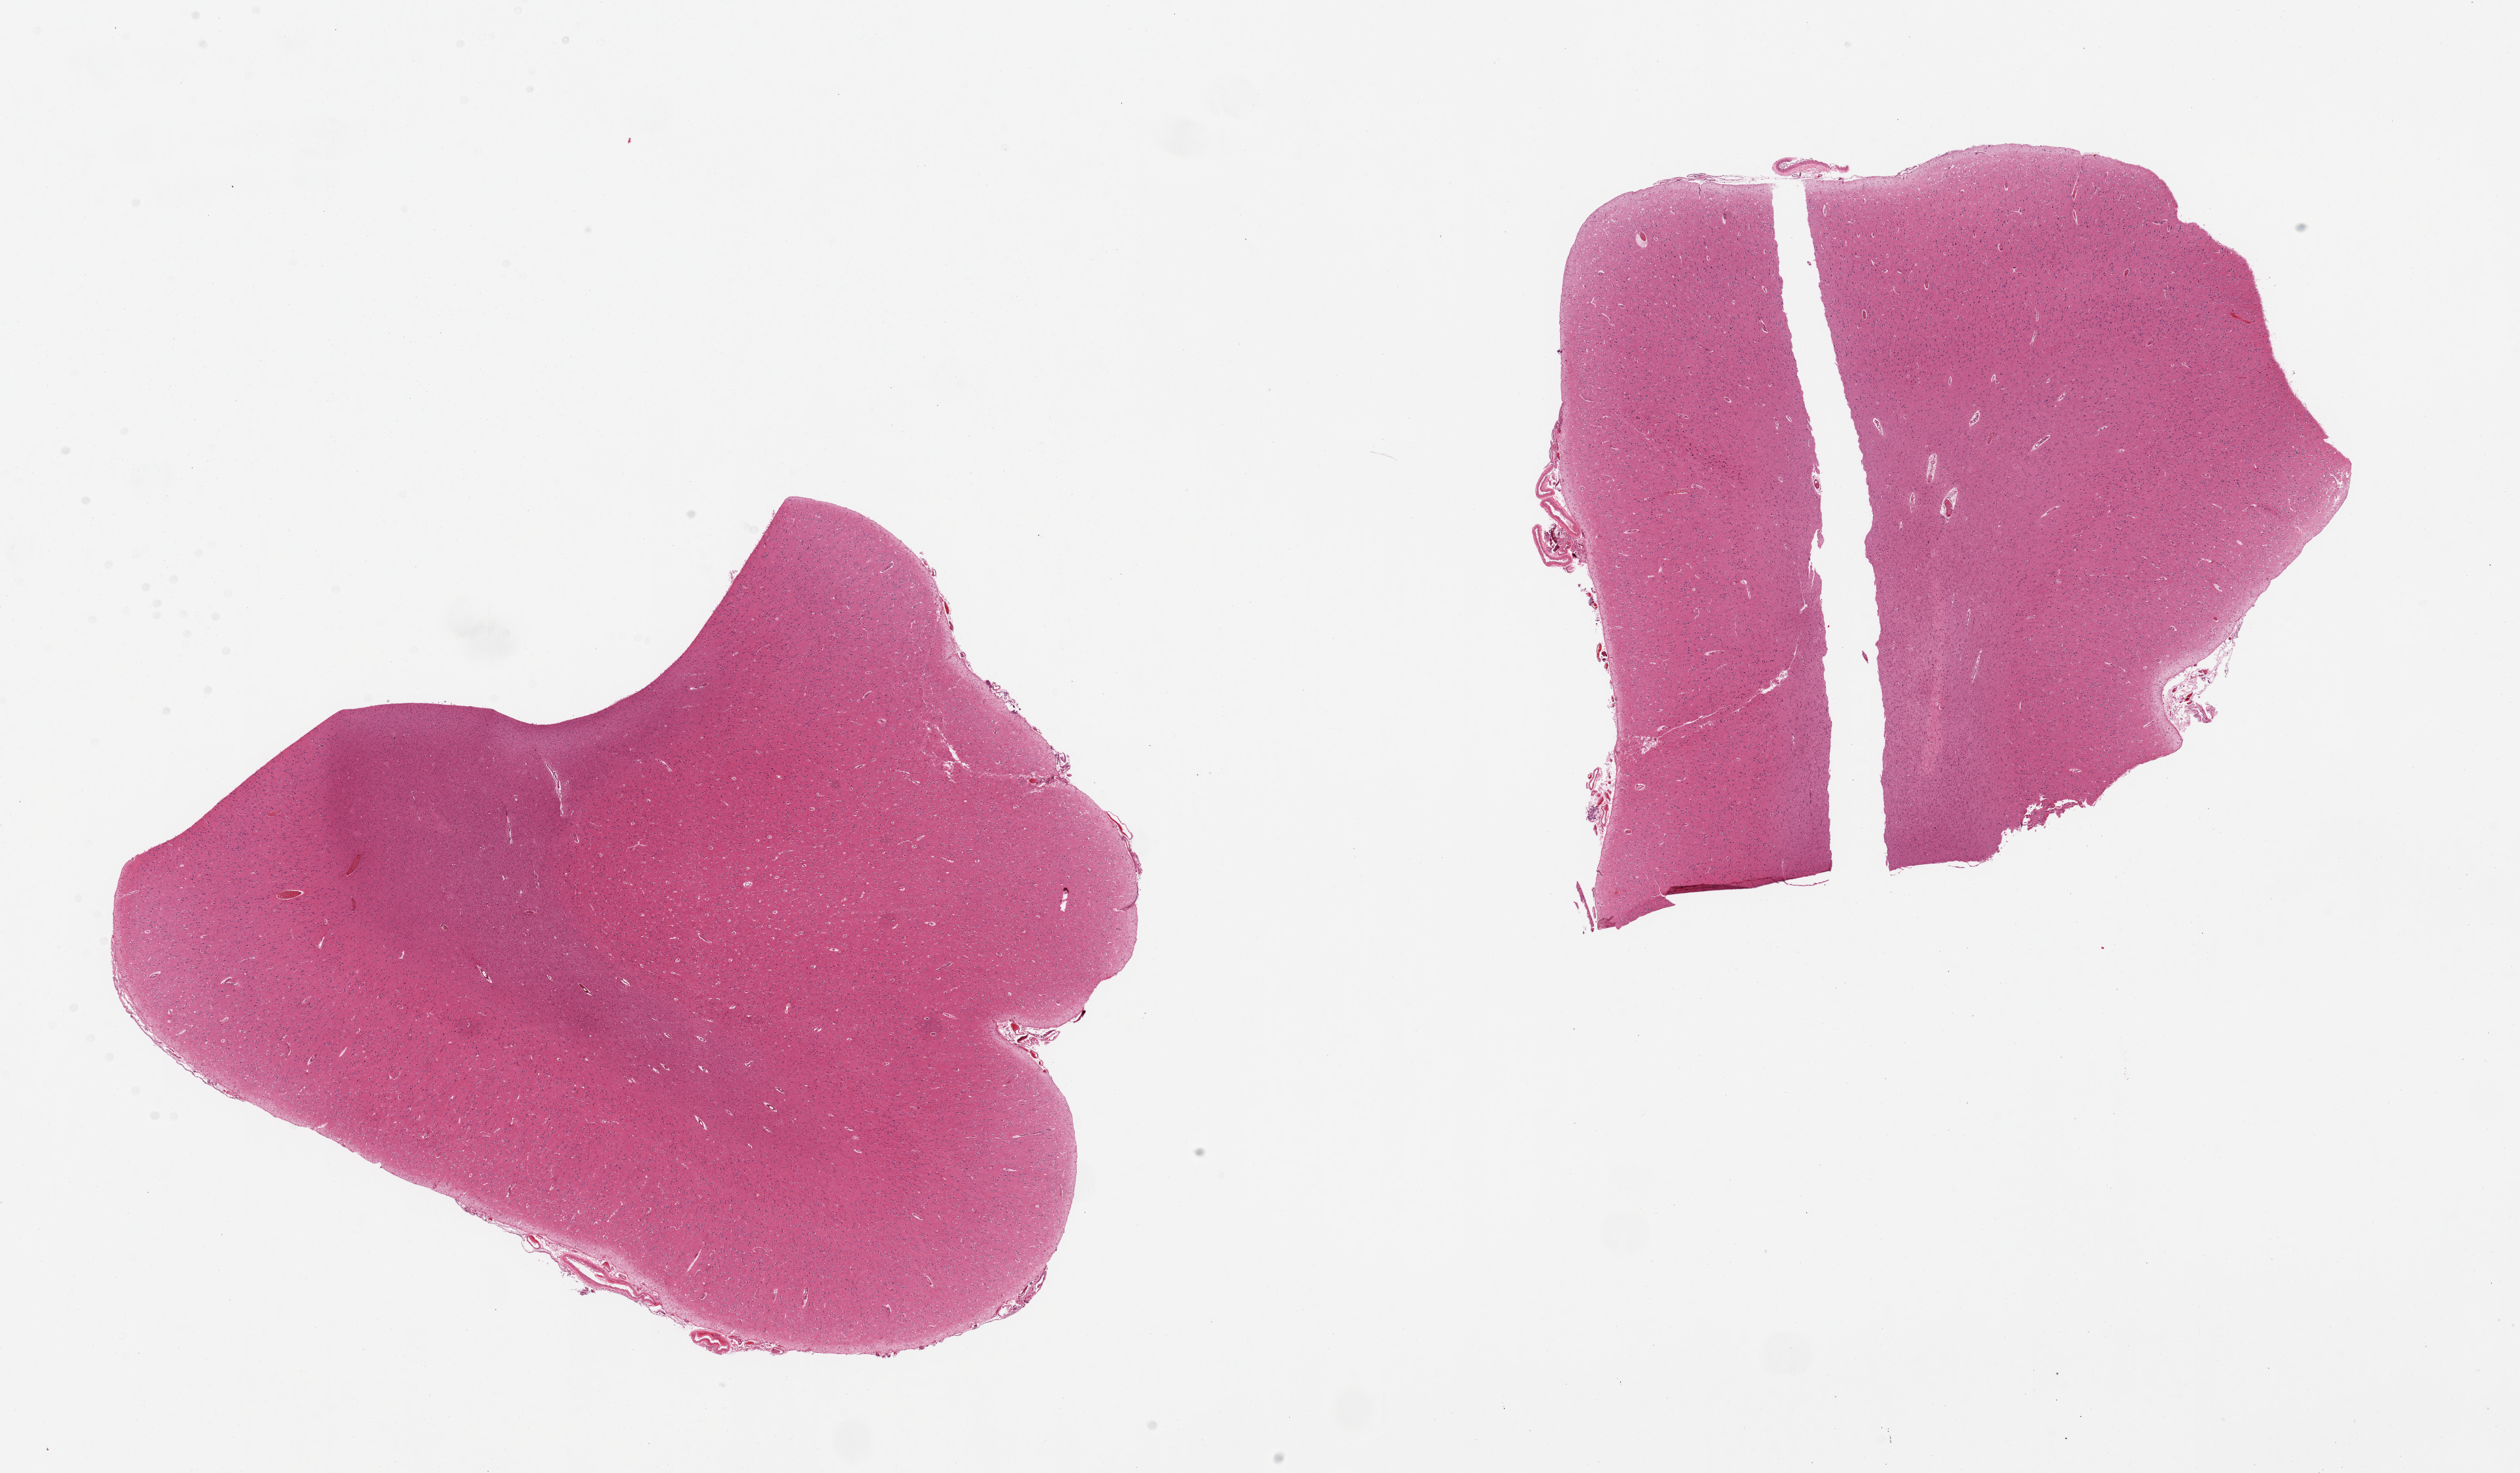
Digitized H&E-stained section, brightfield, low-resolution overview of the scanned area, about 30.5 x 17.8 mm. PAXgene-fixed, paraffin-embedded tissue. Sampled site (target tissue): cerebral cortex. Tissue donor sample.
* reviewer comment on this tissue sample: 2 pieces, no abnormalities